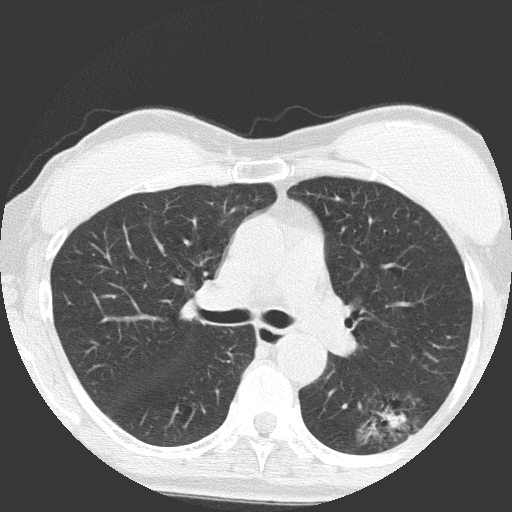
Low-dose screening chest CT, axial slice, baseline screening round, lung window (W 1500 / L -600 HU), 2 mm slice thickness, lung (sharp) reconstruction kernel (FC51), 120 kVp, slice 56 of 149 in the series. Female, age 64 years at enrolment.
Expert-annotated lung lesion, bounding box [x1, y1, x2, y2] px = [341, 389, 427, 461]. Screening reader's record for this exam (one nodule recorded; not confirmed to be the boxed lesion): non-calcified nodule or mass ≥4 mm, right upper lobe, 4 × 4 mm, poorly defined margins, ground glass attenuation. Note: the box lies in the patient's left hemithorax on this image, whereas the reader's record names the right lung; they may be different findings.